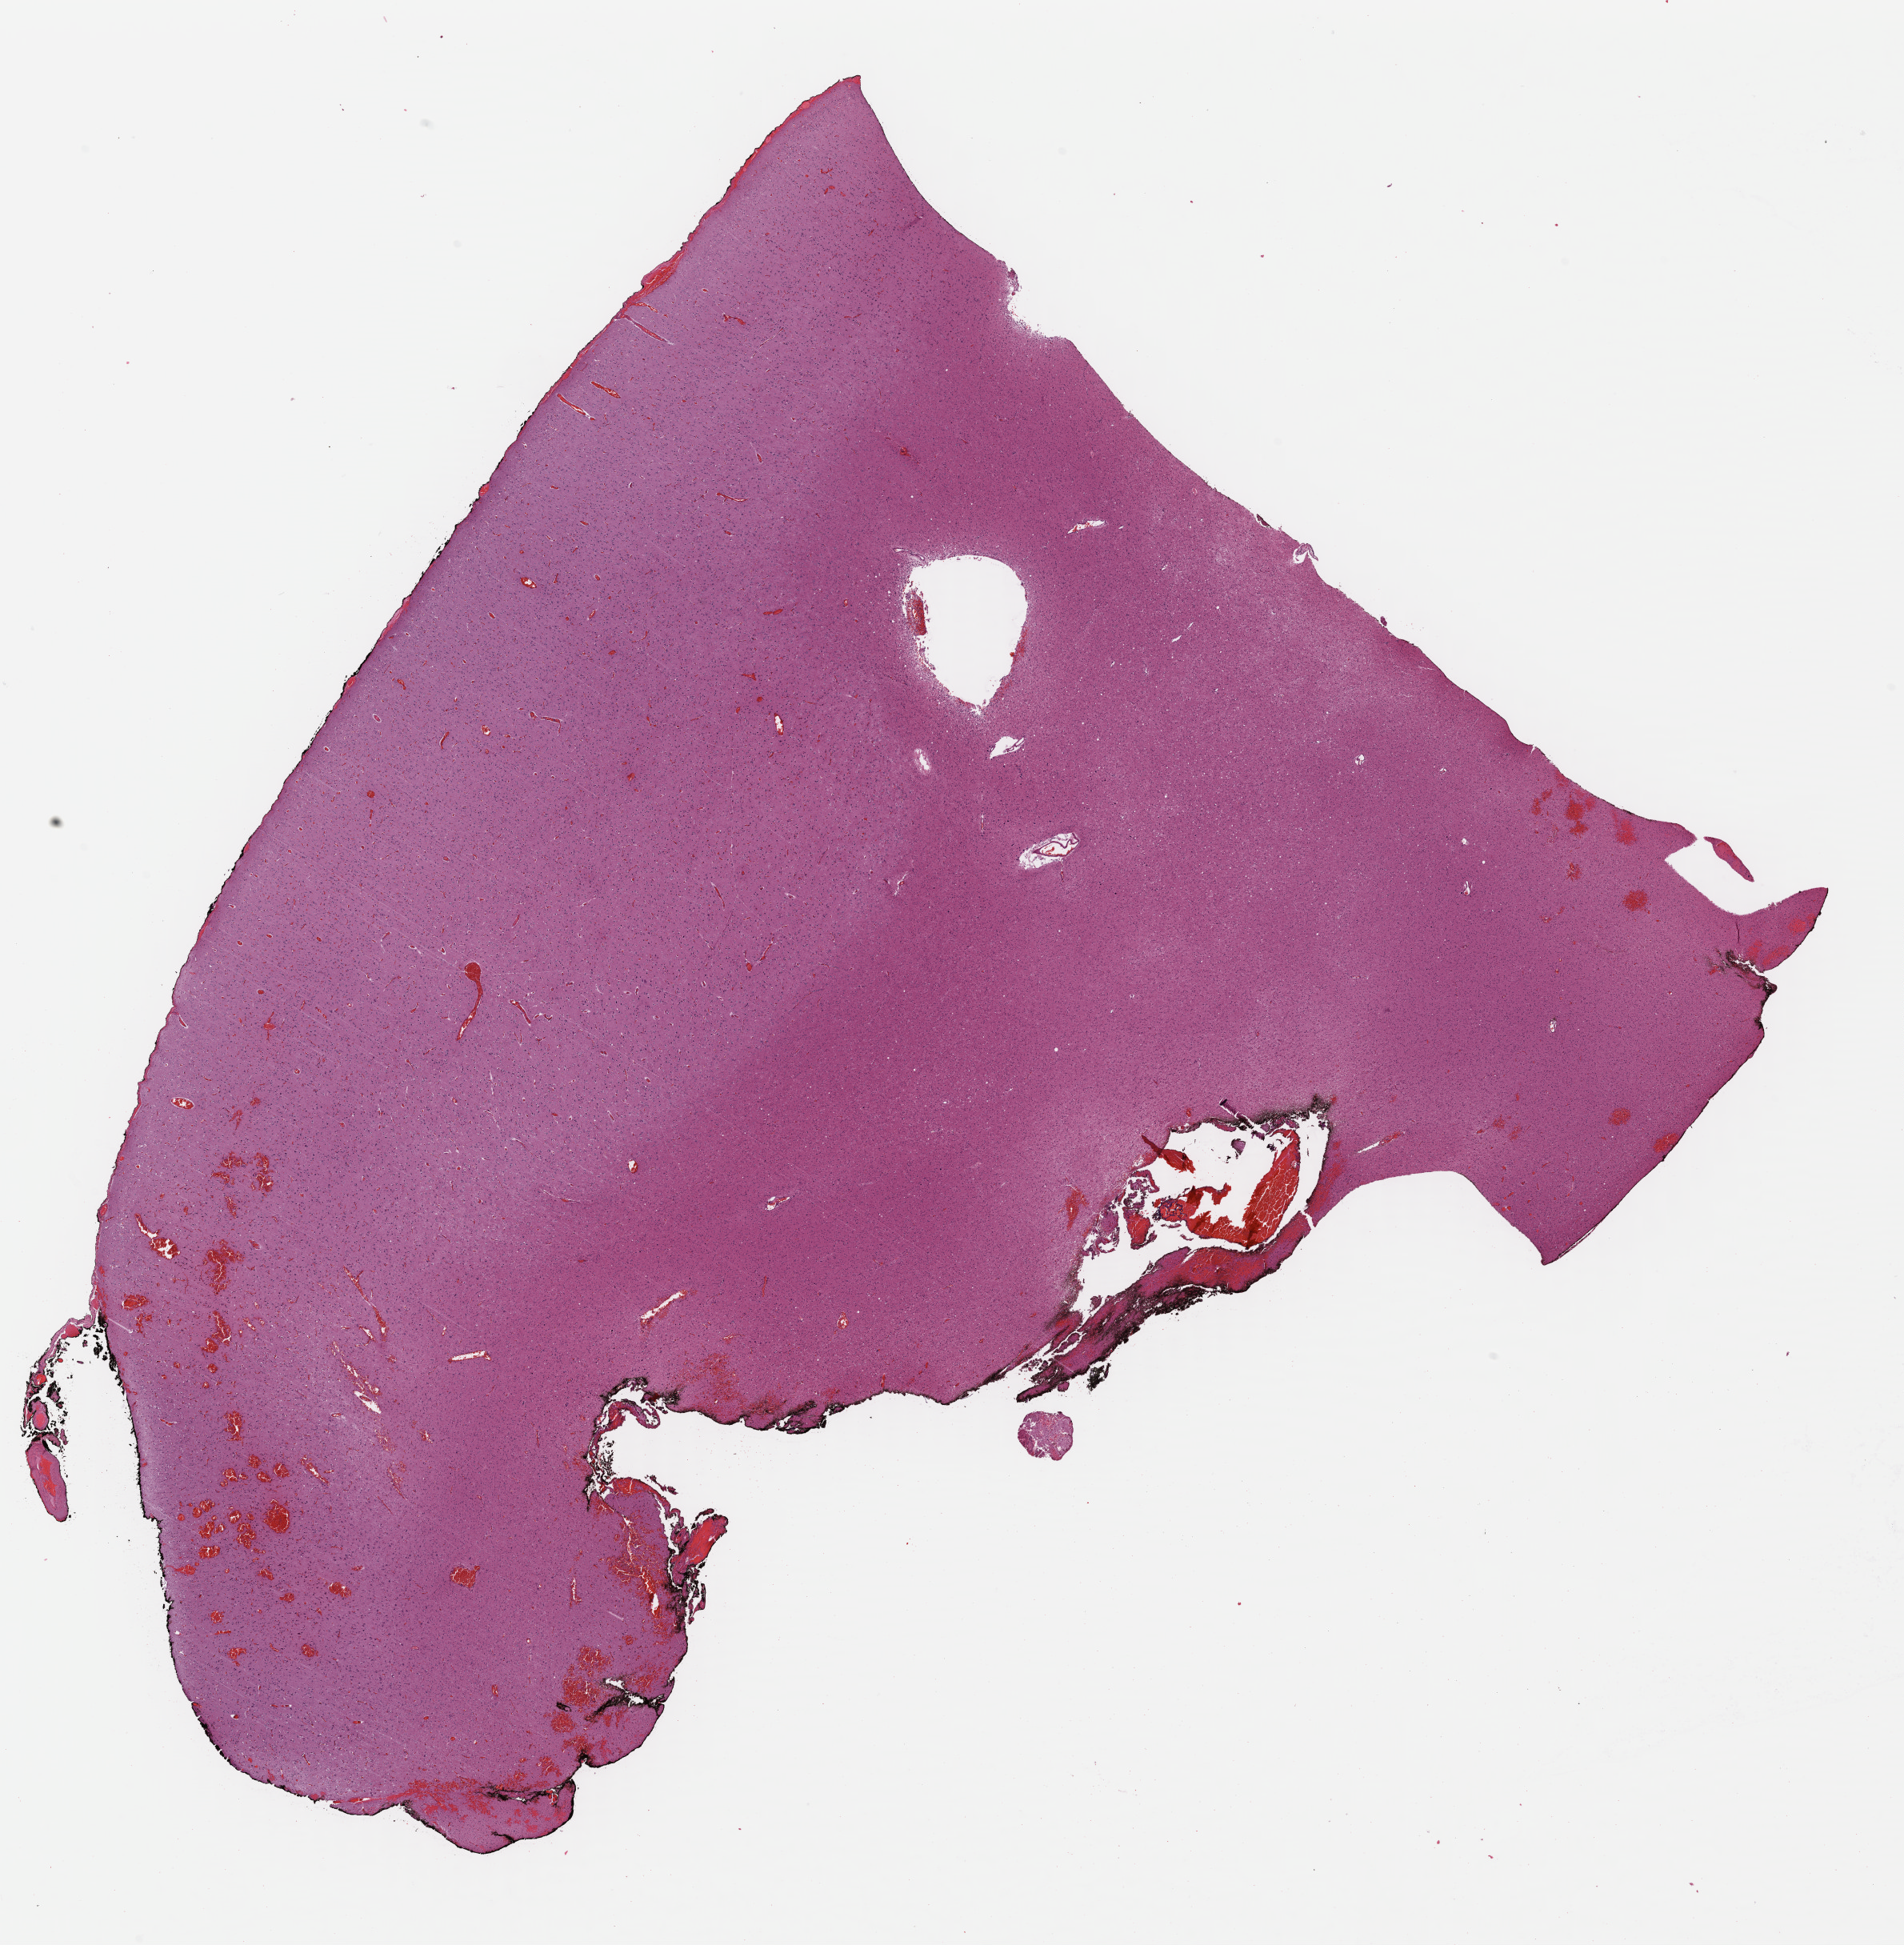
Digitized H&E tissue section (whole slide), low-resolution overview of the scanned area, about 18.7 x 19.1 mm (acquisition: 40x scan). Formalin-fixed paraffin-embedded (FFPE) diagnostic section. Primary tumour sample from the brain. Female patient; age at initial diagnosis 61 years. Histologic grade: G2 (moderately differentiated).
Diagnosis: Astrocytoma, NOS.